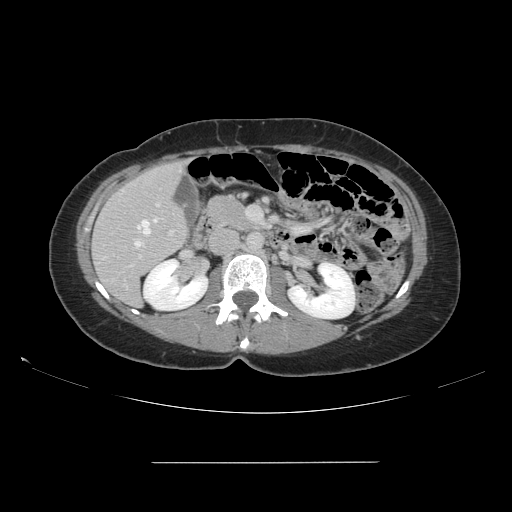
Contrast-enhanced abdominal CT, one axial slice. Slice 72 of 151 in the series (ordered by position). Soft-tissue window (W 400 / L 40 HU). 2.5 mm slice thickness. 512 × 512 image matrix, field of view 421 × 421 mm. Female patient, age 46 years. Case-level facts recorded for this patient, not image findings: diagnosis: colorectal cancer liver metastases, imaged before liver resection; multiple liver metastases: yes; largest metastasis: 3 cm; disease in both lobes: yes.
Structures marked on this image (expert manual segmentation):
- hepatic veins: box from (x=134, y=219) to (x=158, y=247) px
- liver: (x=93, y=162)–(x=187, y=306)
- planned liver remnant (the part of the liver to remain after resection): (x=93, y=162)–(x=187, y=307)
- portal vein (with intrahepatic branches): (x=129, y=202)–(x=174, y=267)